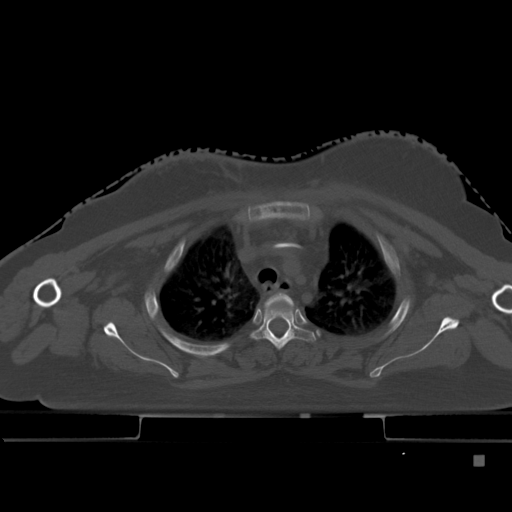
CT including the spine, one axial slice; slice 348 of 495 in the series (ordered by position); bone window (W 1800 / L 400 HU); 512 × 512 image matrix. Patient: female, 33 years. Case-level facts recorded for this patient, not image findings: primary cancer: breast; vertebrae with lytic lesions (as recorded): T1.
Outlined on this slice (semi-automatic segmentation, software-assisted and operator-edited):
- T2 vertebra: box from (x=266, y=292) to (x=294, y=308) px
- T3 vertebra: (x=252, y=307)–(x=317, y=350)